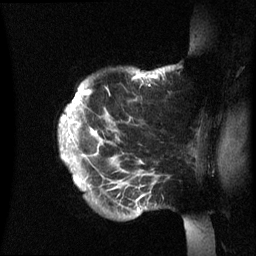
Breast MRI (dynamic contrast-enhanced), one sagittal slice; position 52 of 60 along the scan axis; dynamic contrast-enhanced series, image 2 of 3 at this slice position (ordered by acquisition); 1.5 T; TE 4.2 ms, TR 8.4 ms; 256 × 256 image matrix. Female patient, age 48 years.
Outlined on this slice (semi-automatic segmentation, software-assisted and operator-edited):
- analysis volume of interest (the breast-tissue region the enhancement analysis was run in; not a lesion): bounding box (x1, y1, x2, y2) in pixels: (60, 67, 199, 236)
- tumour enhancement mask (voxels above the 70 % enhancement threshold inside the analysis volume of interest): (60, 68, 164, 210)